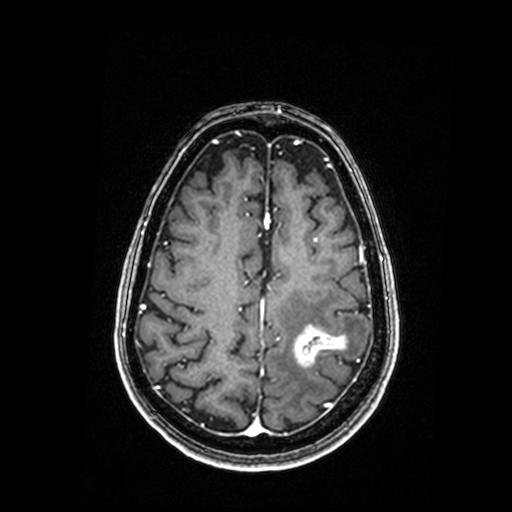
Brain MRI from a brain-tumour surgery series, one axial slice. Slice 59 of 192 in the series (ordered by position). T1-weighted post-contrast. 0.98 mm slice thickness. 512 × 512 image matrix, field of view 250 × 250 mm. Case-level facts recorded for this patient, not image findings: histopathology: Metastastic Carcinoma, Poorly Differentiated; tumour location: Left Parietal.
Annotated regions visible in this slice (outlined manually by an expert reader):
- tumour: bounding box <294,329,346,367> (left, top, right, bottom; pixels)